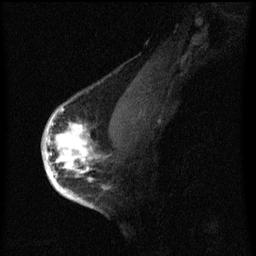
Breast MRI (dynamic contrast-enhanced), one sagittal slice. Slice 41 of 60 in the series (ordered by position). Dynamic contrast-enhanced series, image 2 of 3 at this slice position (ordered by acquisition). 1.5 T. TE 4.2 ms, TR 8 ms. 2 mm slice thickness. 256 × 256 image matrix. Female patient, age 56 years.
Outlined on this slice (semi-automatic segmentation, software-assisted and operator-edited):
- analysis volume of interest (the breast-tissue region the enhancement analysis was run in; not a lesion): bounding box [x1, y1, x2, y2] px = [44, 110, 109, 193]
- tumour enhancement mask (voxels above the 70 % enhancement threshold inside the analysis volume of interest): [44, 110, 101, 193]